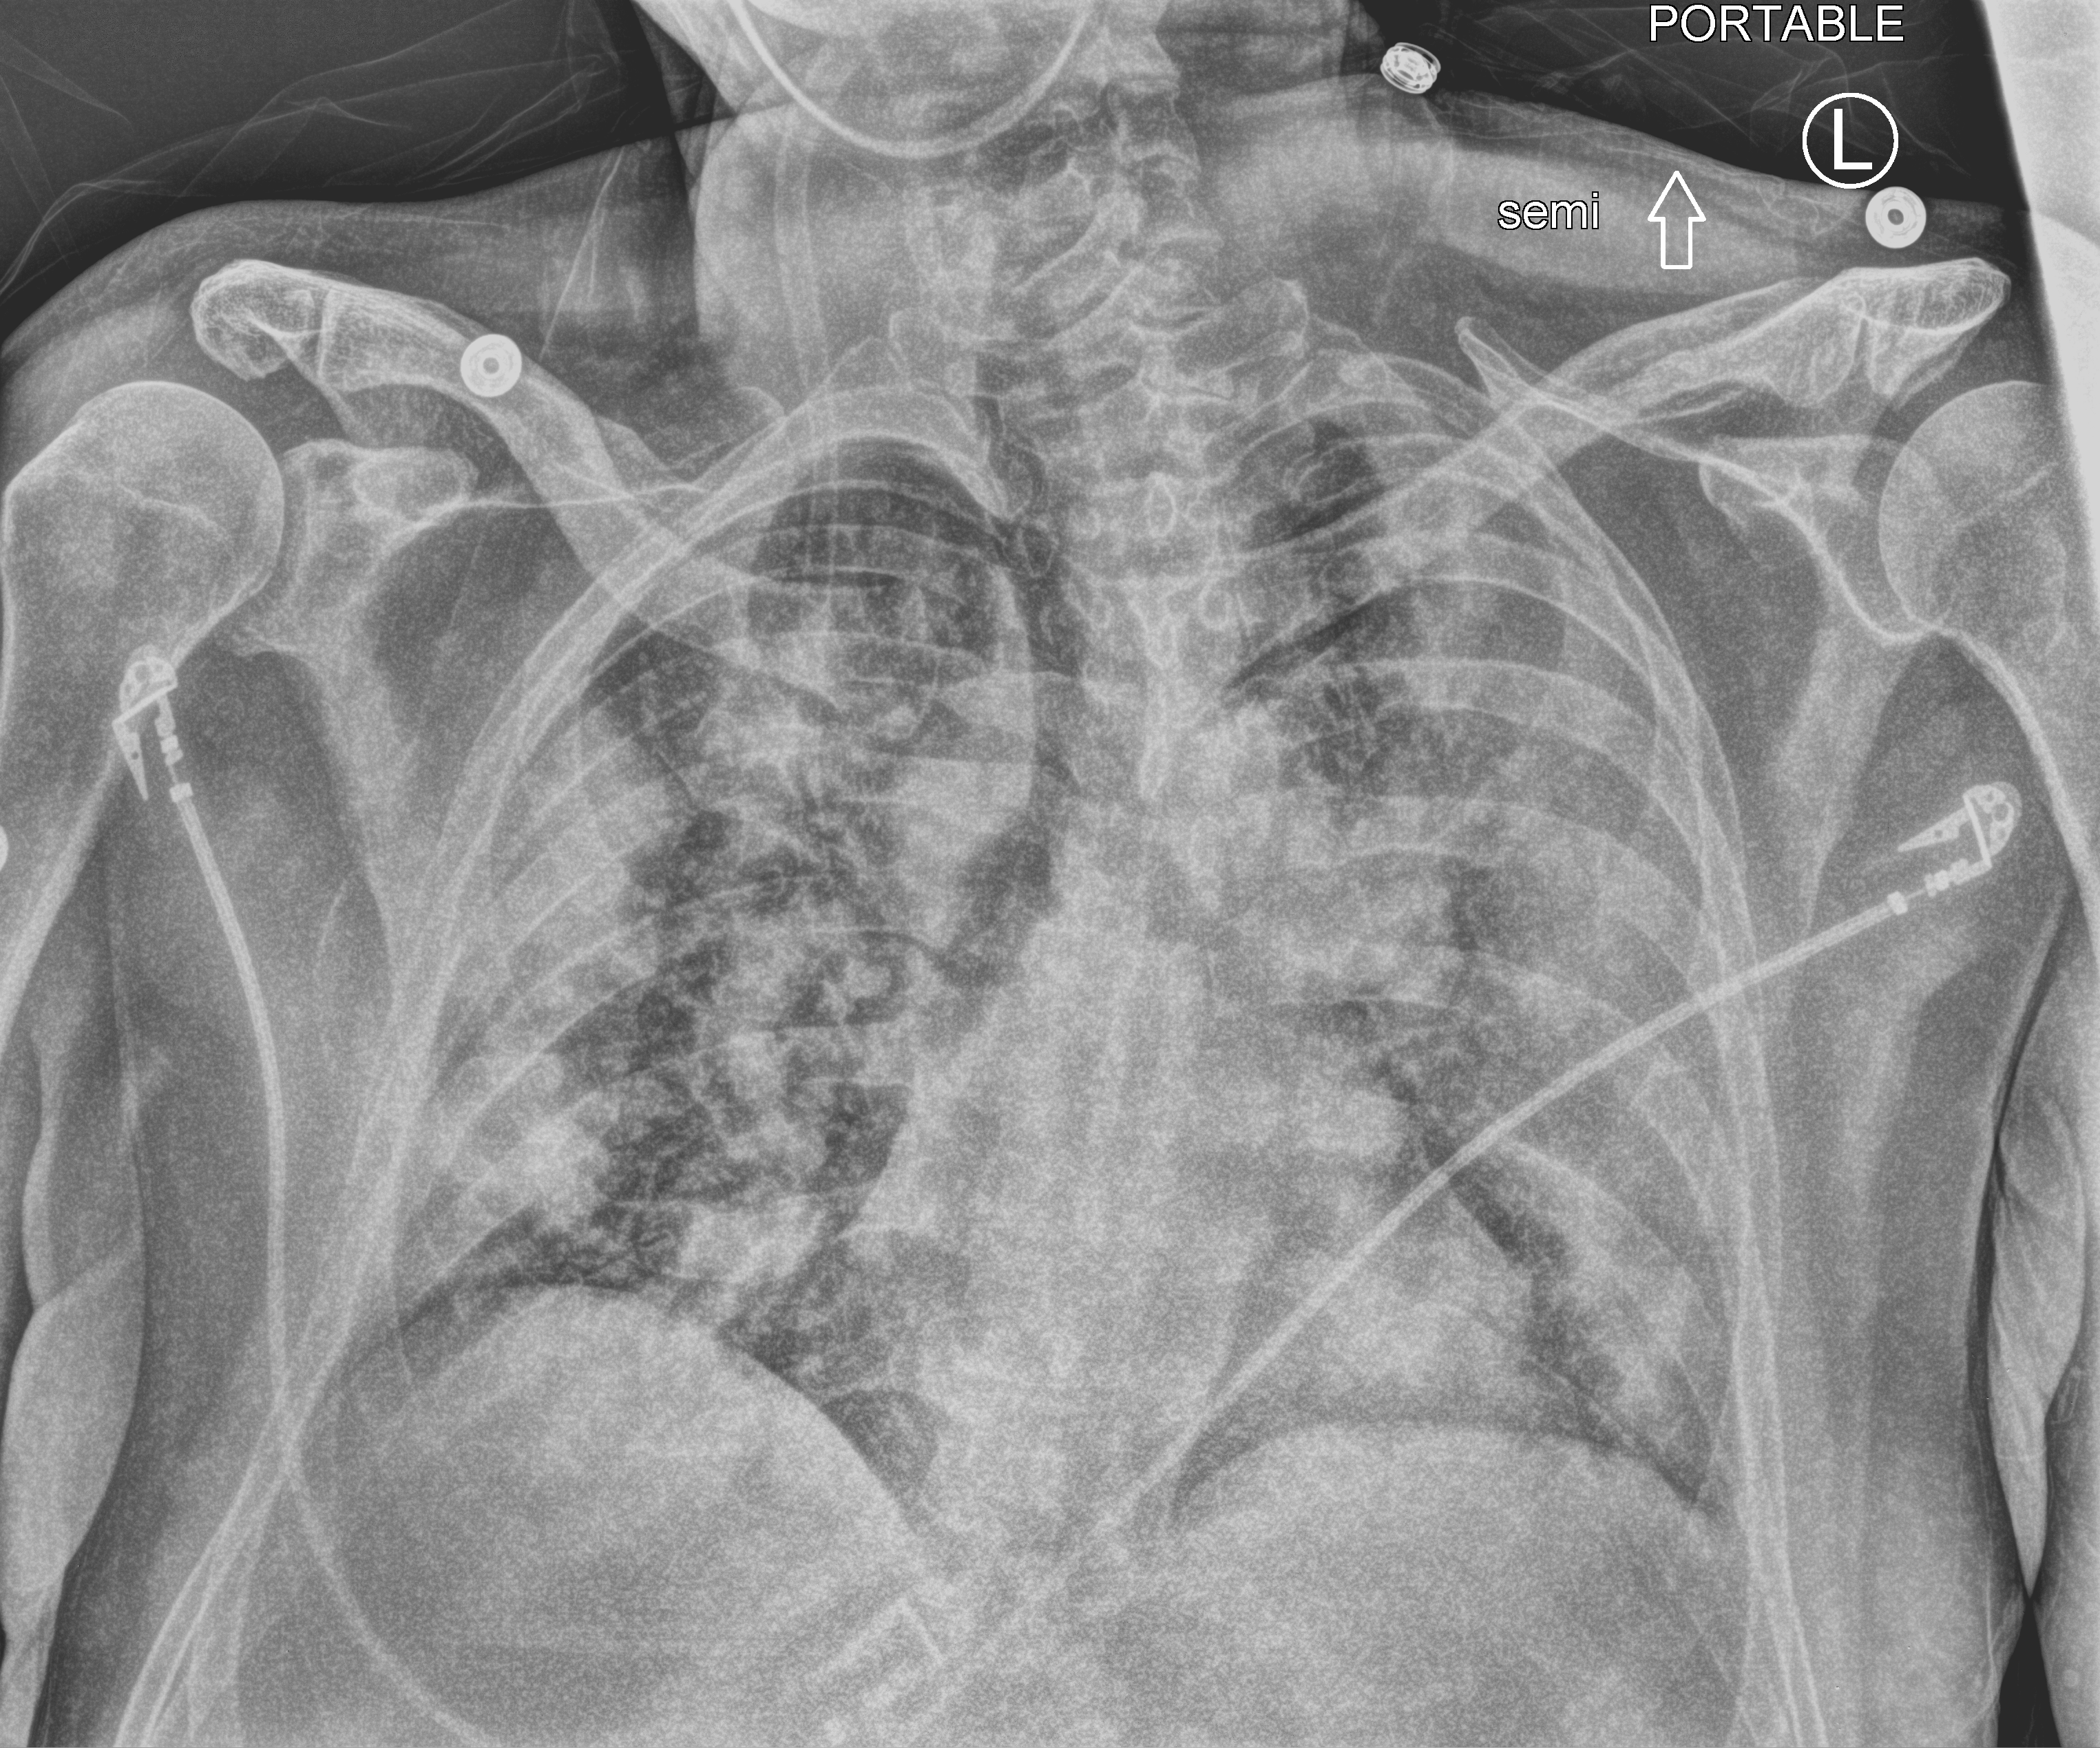
Chest X-ray (portable); anteroposterior (AP) projection. Male patient hospitalised with COVID-19, age 18–59 years.
Admission-level facts for this patient (not findings on this image; timing relative to this image not recorded): mechanically ventilated during this hospital stay: yes; chronic kidney disease (admission record): no; hypertension (admission record): yes.